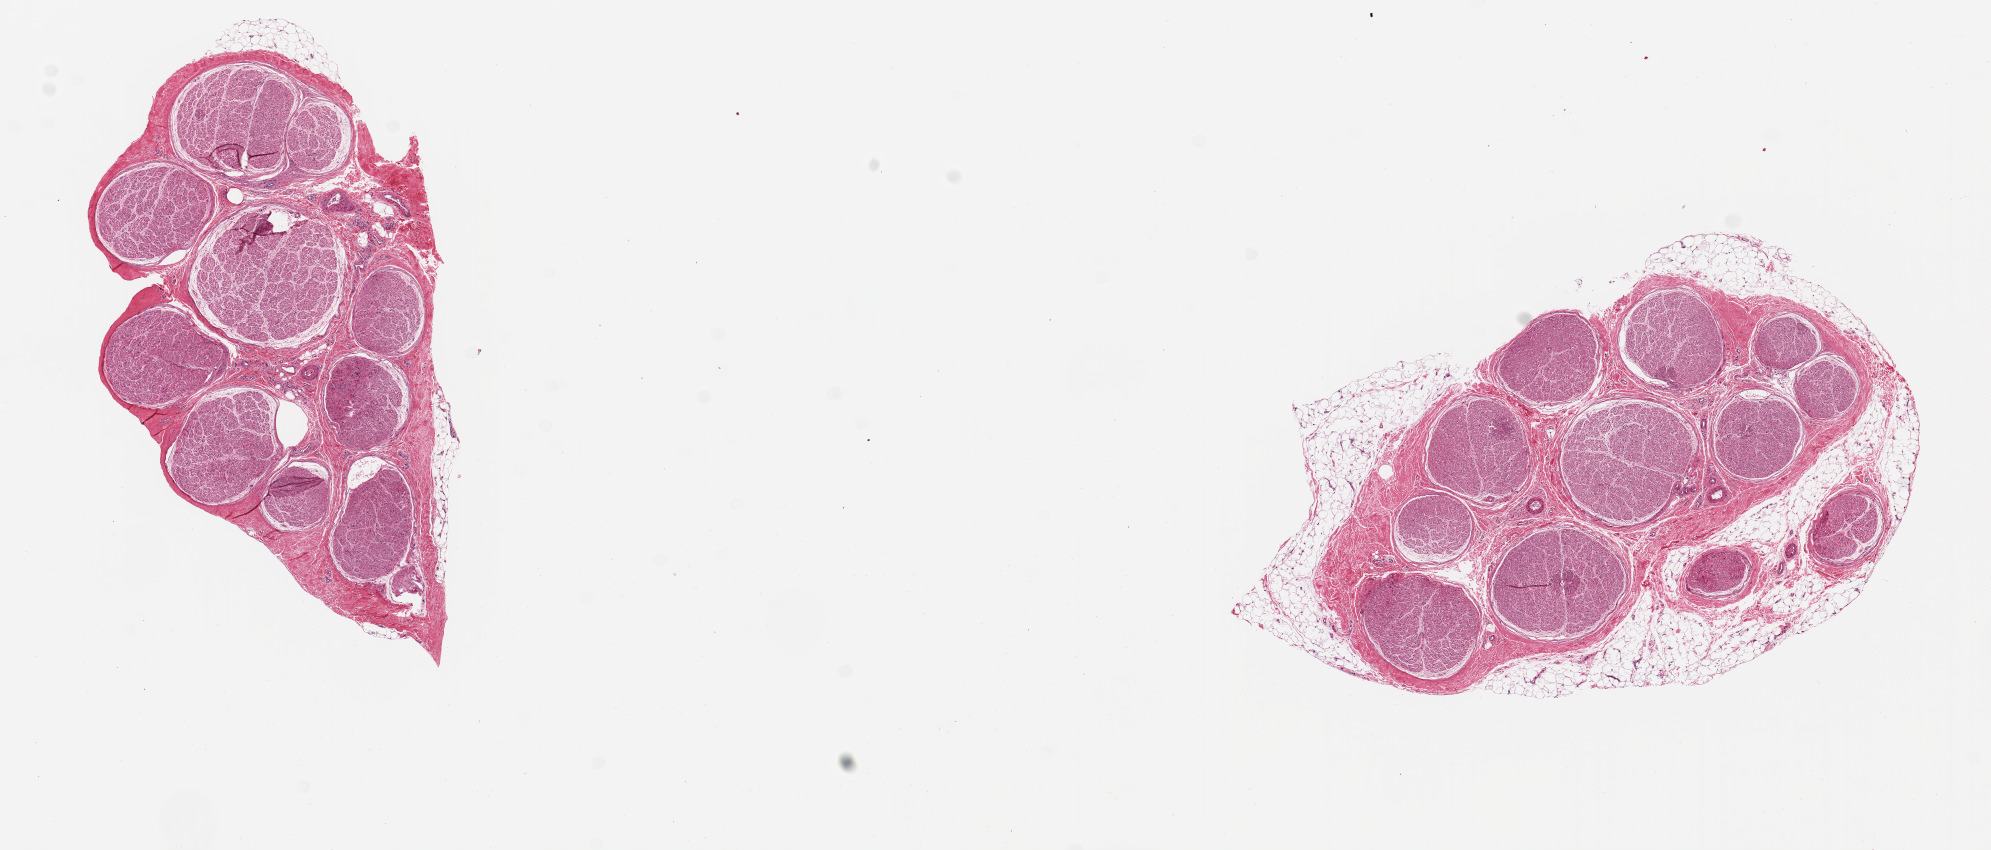
H&E whole-slide image — low-resolution overview of the scanned area, about 15.8 x 6.7 mm. PAXgene-fixed, paraffin-embedded tissue. Section of tibial nerve (target tissue). Donor tissue sample. Male donor.
Pathologist's review note for this sample: 2 pieces ~4mm d; Nerve tissue.